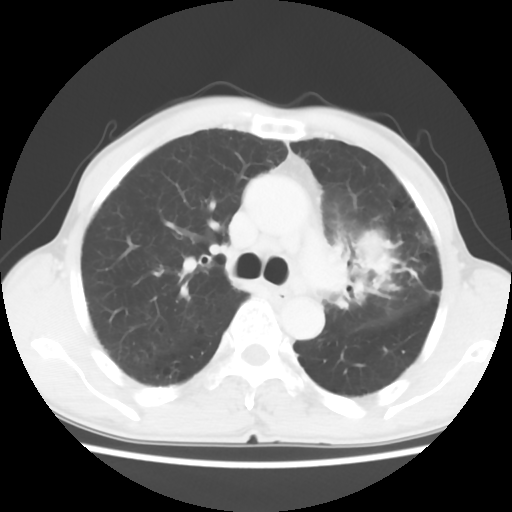
Chest CT, one axial slice. Position 39 of 60 along the scan axis. Reconstruction kernel STANDARD. 120 kVp. Lung window (W 1500 / L -600 HU). 512 × 512 image matrix, field of view 308 × 308 mm. Male patient, age 64 years. From the clinical record (not read from this slice): clinical TNM (as recorded): T3 N3 M0; histopathological grade: G3.
Annotated regions visible in this slice (rectangle marked by the reading radiologist):
- lung tumour (recorded histology: adenocarcinoma): bounding box (x1, y1, x2, y2) in pixels: (338, 220, 414, 308)